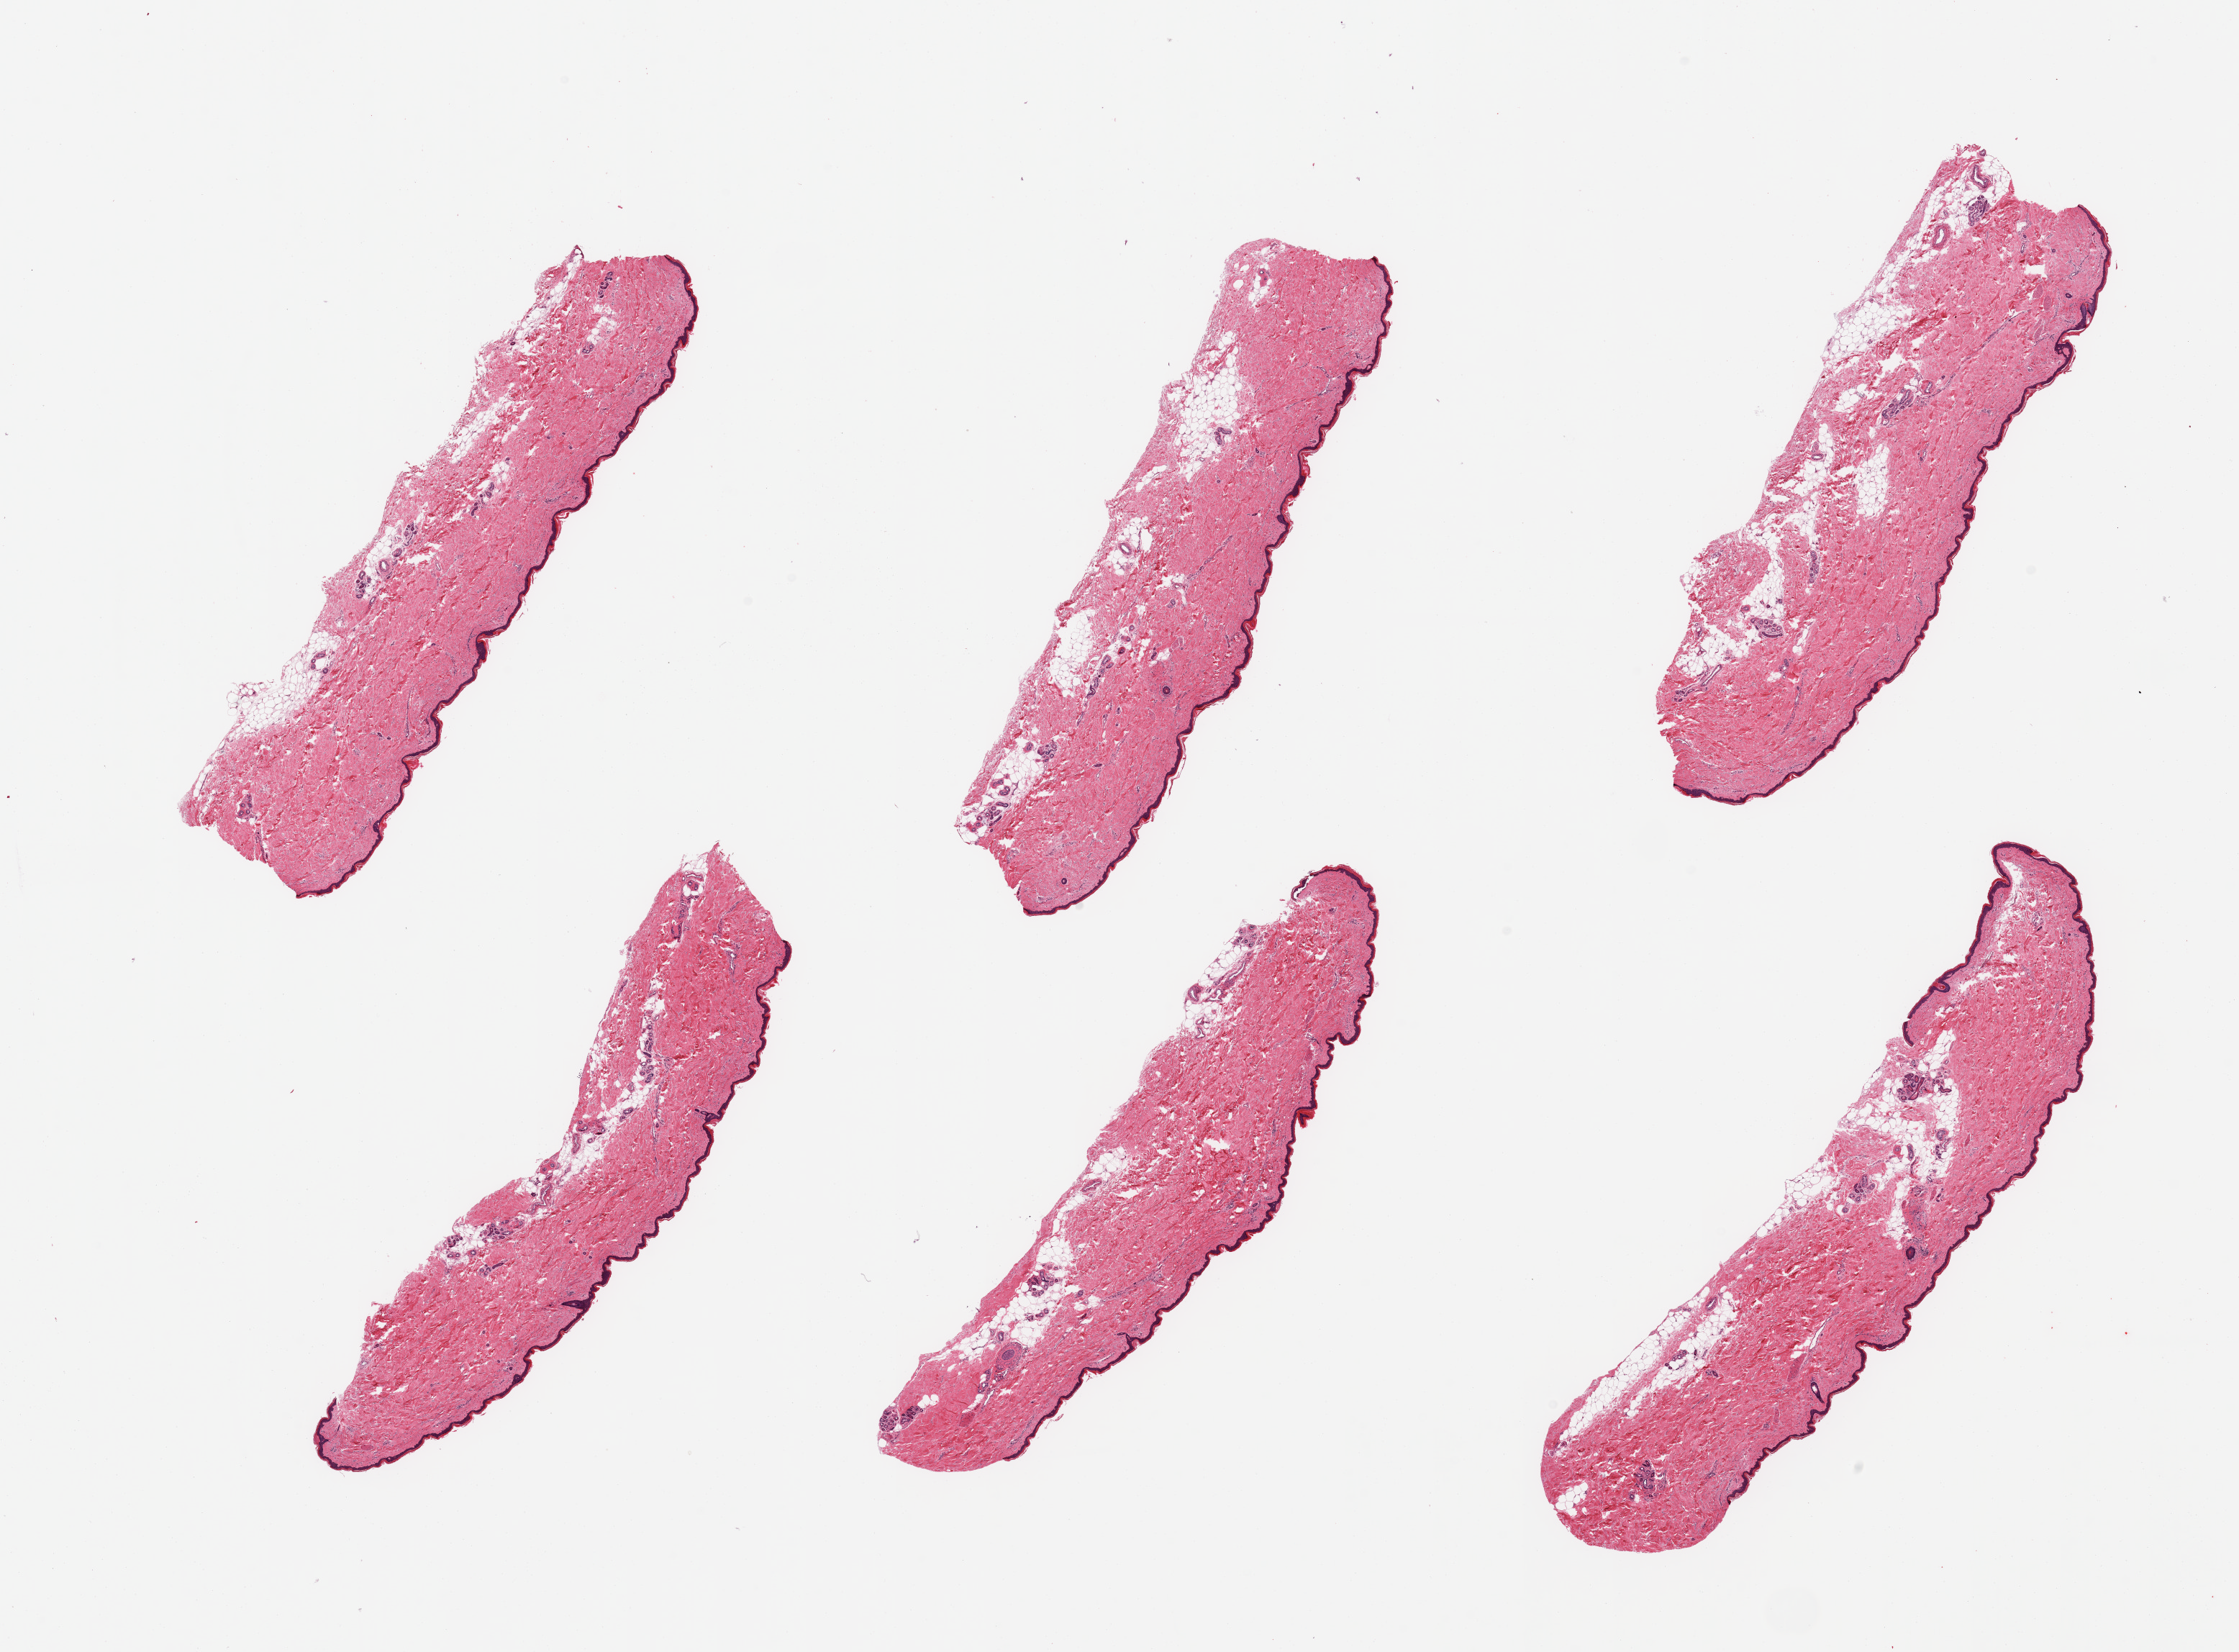
Whole-slide image, haematoxylin and eosin stain — a low-resolution overview of the entire scanned area, about 24.6 x 18.2 mm (from a 20x scan); PAXgene-fixed paraffin-embedded (PFPE) section; sampled site (target tissue): skin of lower leg; tissue donor sample.
Pathologist's review note for this sample: 6 pieces moderate amounts of dermal fat; squamous epithelium is ~35-40 microns.